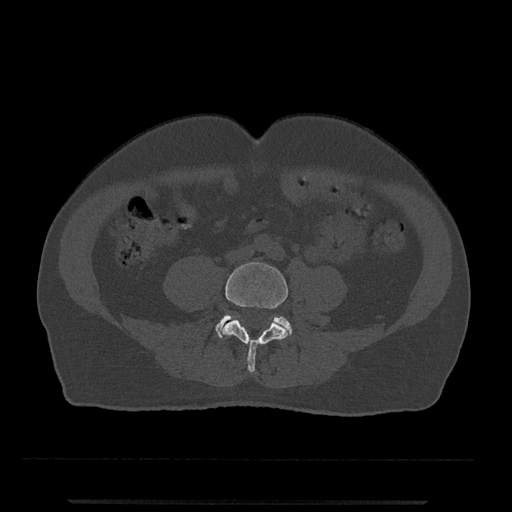
CT including the spine, one axial slice; position 117 of 797 along the scan axis; reconstruction kernel Br40s/3; 120 kVp; bone window (W 1800 / L 400 HU); 512 × 512 image matrix, field of view 419 × 419 mm. Patient: male, 63 years. From the clinical record (not read from this slice): primary cancer: prostate.
Annotated regions visible in this slice (semi-automatic segmentation, software-assisted and operator-edited):
- L4 vertebra: bounding box (x1, y1, x2, y2) in pixels: (222, 262, 288, 373)
- L5 vertebra: (216, 315, 292, 338)